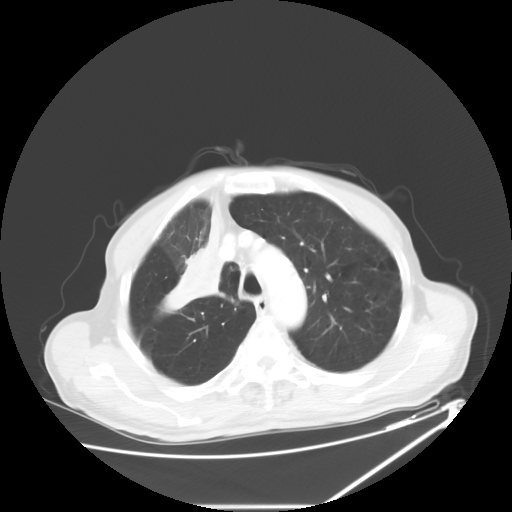
Chest CT, one axial slice. Slice 47 of 60 in the series (ordered by position). 120 kVp. Lung window (W 1500 / L -600 HU). 512 × 512 image matrix, field of view 410 × 410 mm. Male patient, age 73 years. From the clinical record (not read from this slice): clinical TNM (as recorded): T2a N1 M0.
Annotated regions visible in this slice (rectangle marked by the reading radiologist):
- lung tumour (recorded histology: squamous cell carcinoma): bounding box (x1, y1, x2, y2) in pixels: (170, 200, 224, 316)